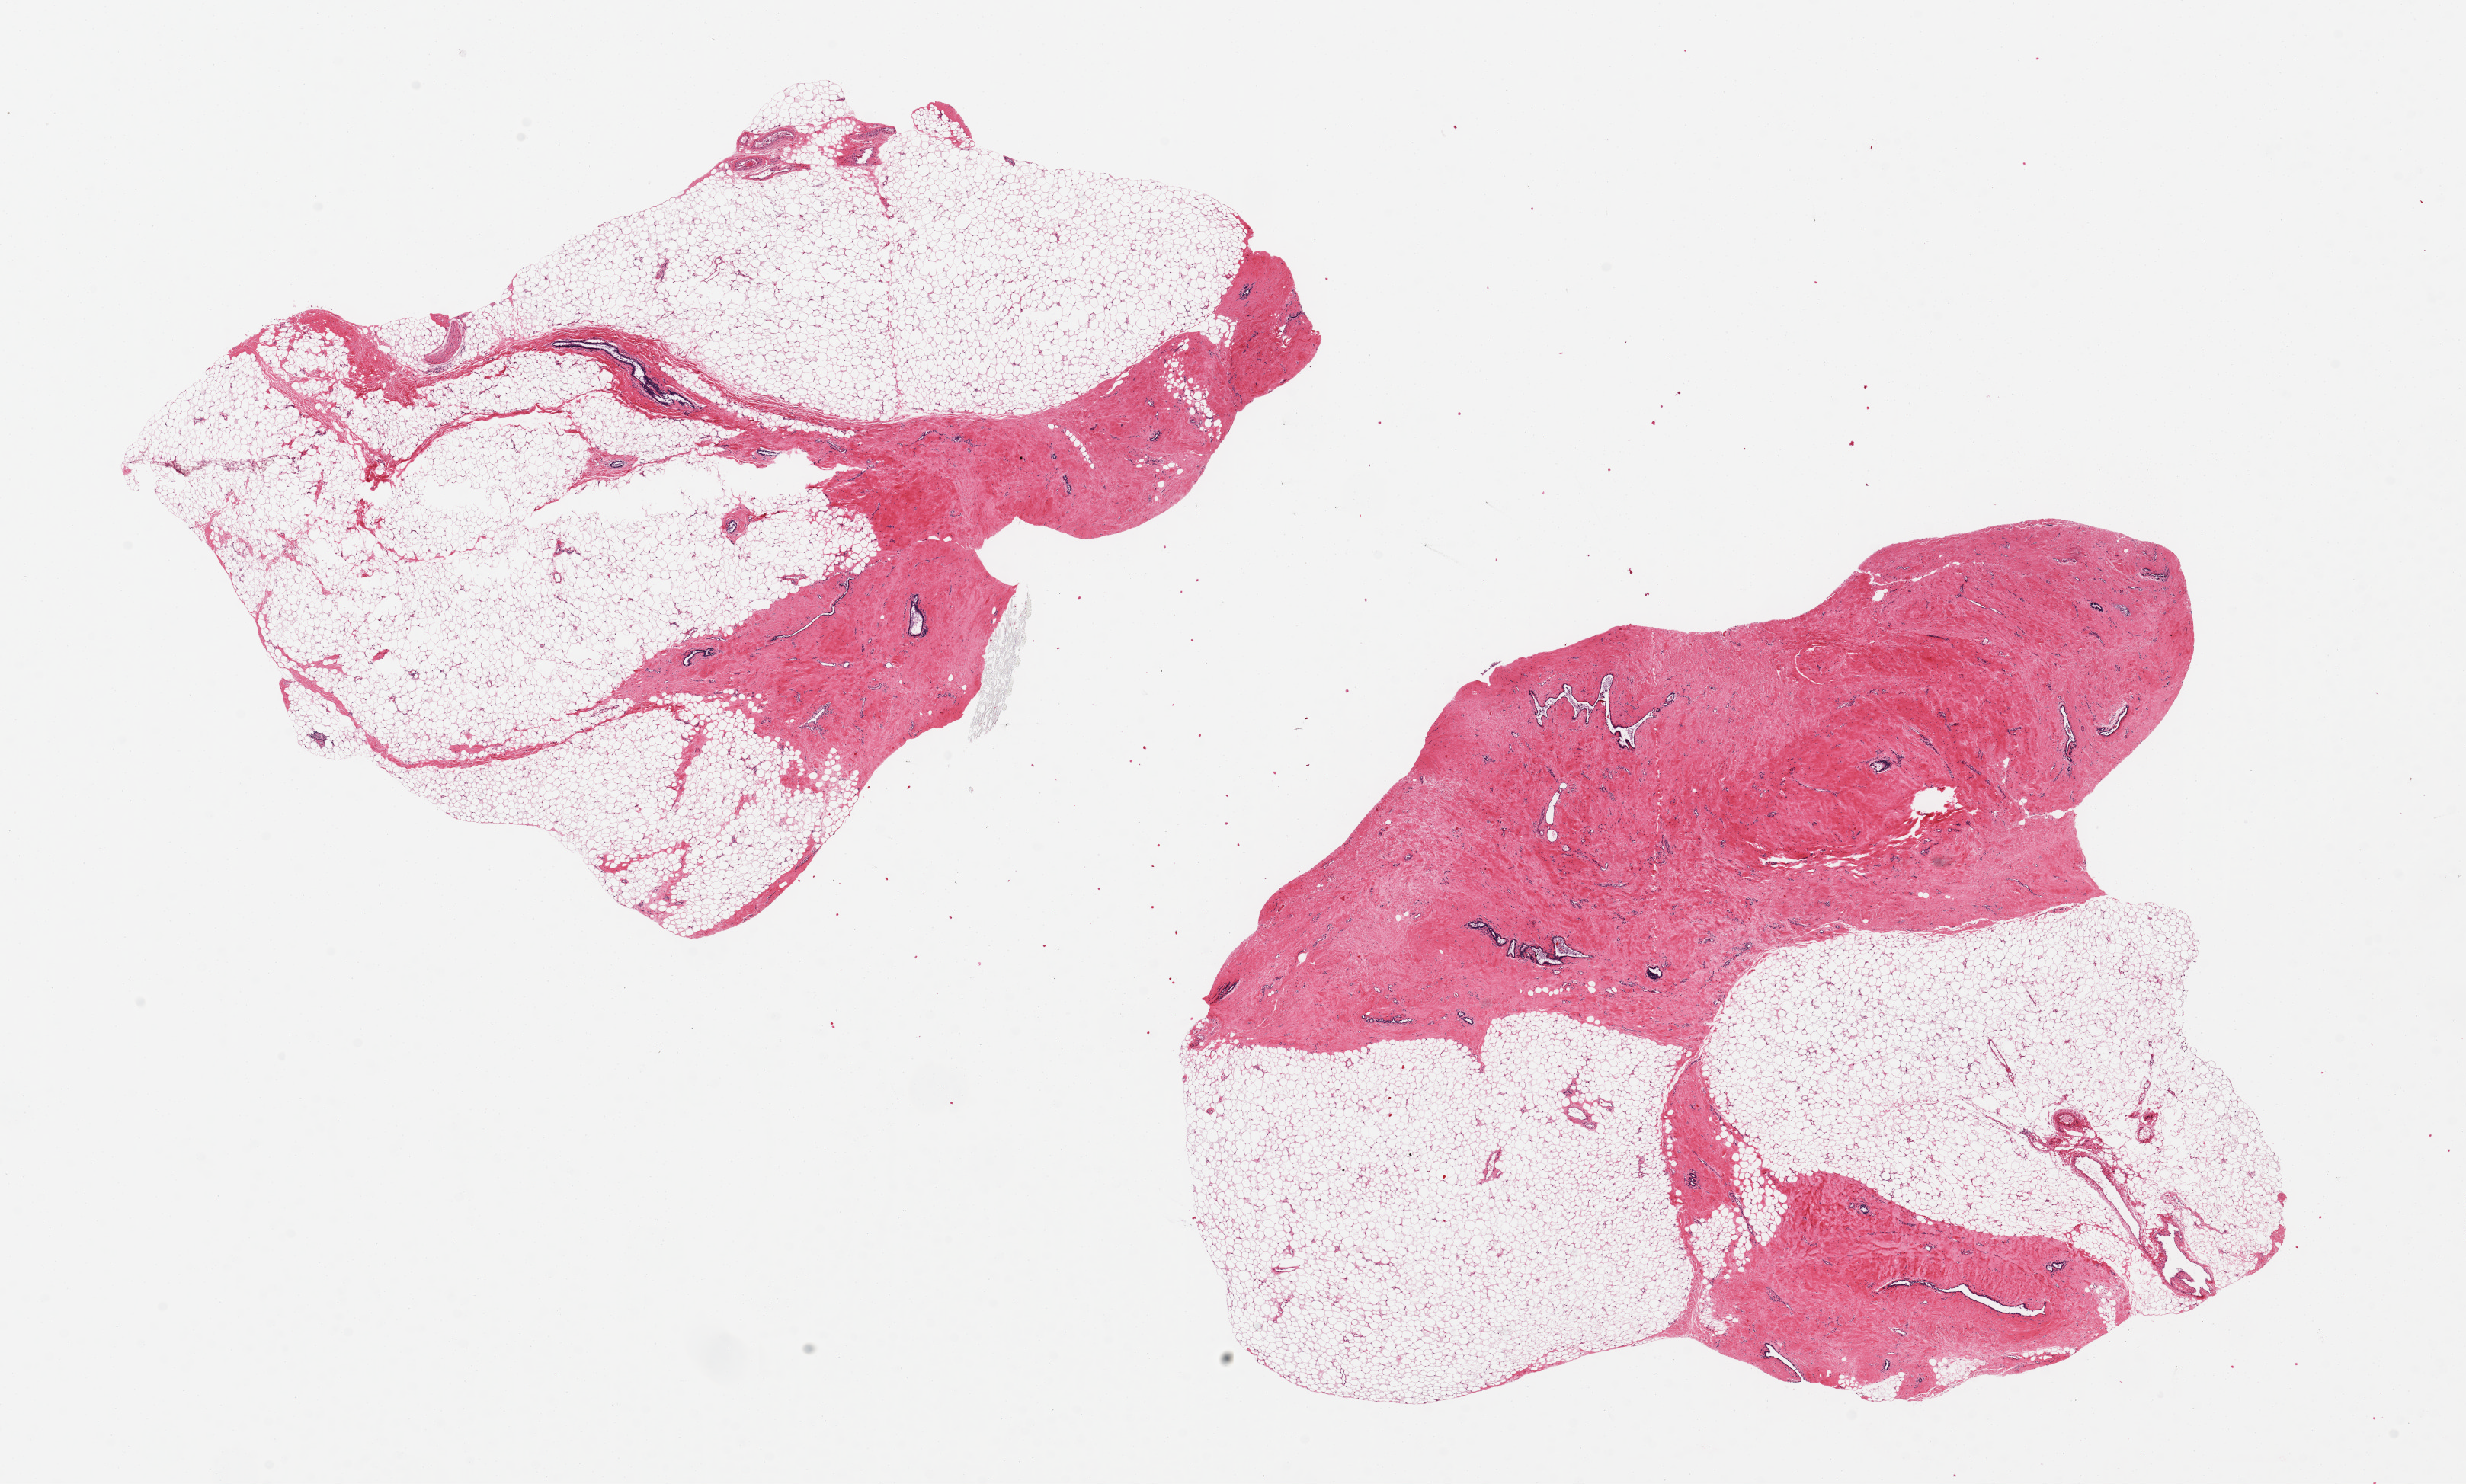
Whole-slide image, hematoxylin and eosin (H&E) stain, a low-resolution overview of the entire scanned area, about 25.6 x 15.4 mm (slide scanned at 20x), PAXgene-fixed, paraffin-embedded tissue, sampled site (target tissue): breast, donor tissue sample. Donor: male.
Review note (as recorded): 2 pieces 10x7 & 9x8 mm; gynecomastia with ductal and fibrous tissue; 80 and 60 % adipose.